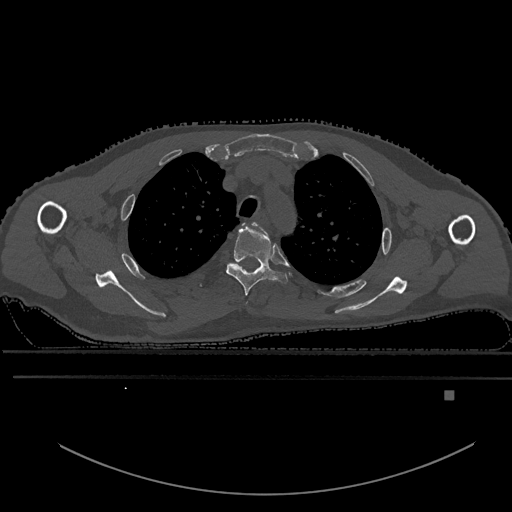
CT including the spine, one axial slice. Position 451 of 969 along the scan axis. Bone window (W 1800 / L 400 HU). 512 × 512 image matrix, field of view 456 × 456 mm. Patient: male, 82 years. Case-level facts recorded for this patient, not image findings: primary cancer: prostate; vertebrae with lytic lesions (as recorded): T11, T9, T8, T2.
Outlined on this slice (semi-automatic segmentation, software-assisted and operator-edited):
- T2 vertebra: bounding box [x1, y1, x2, y2] px = [242, 222, 260, 226]
- T3 vertebra: [225, 222, 288, 295]